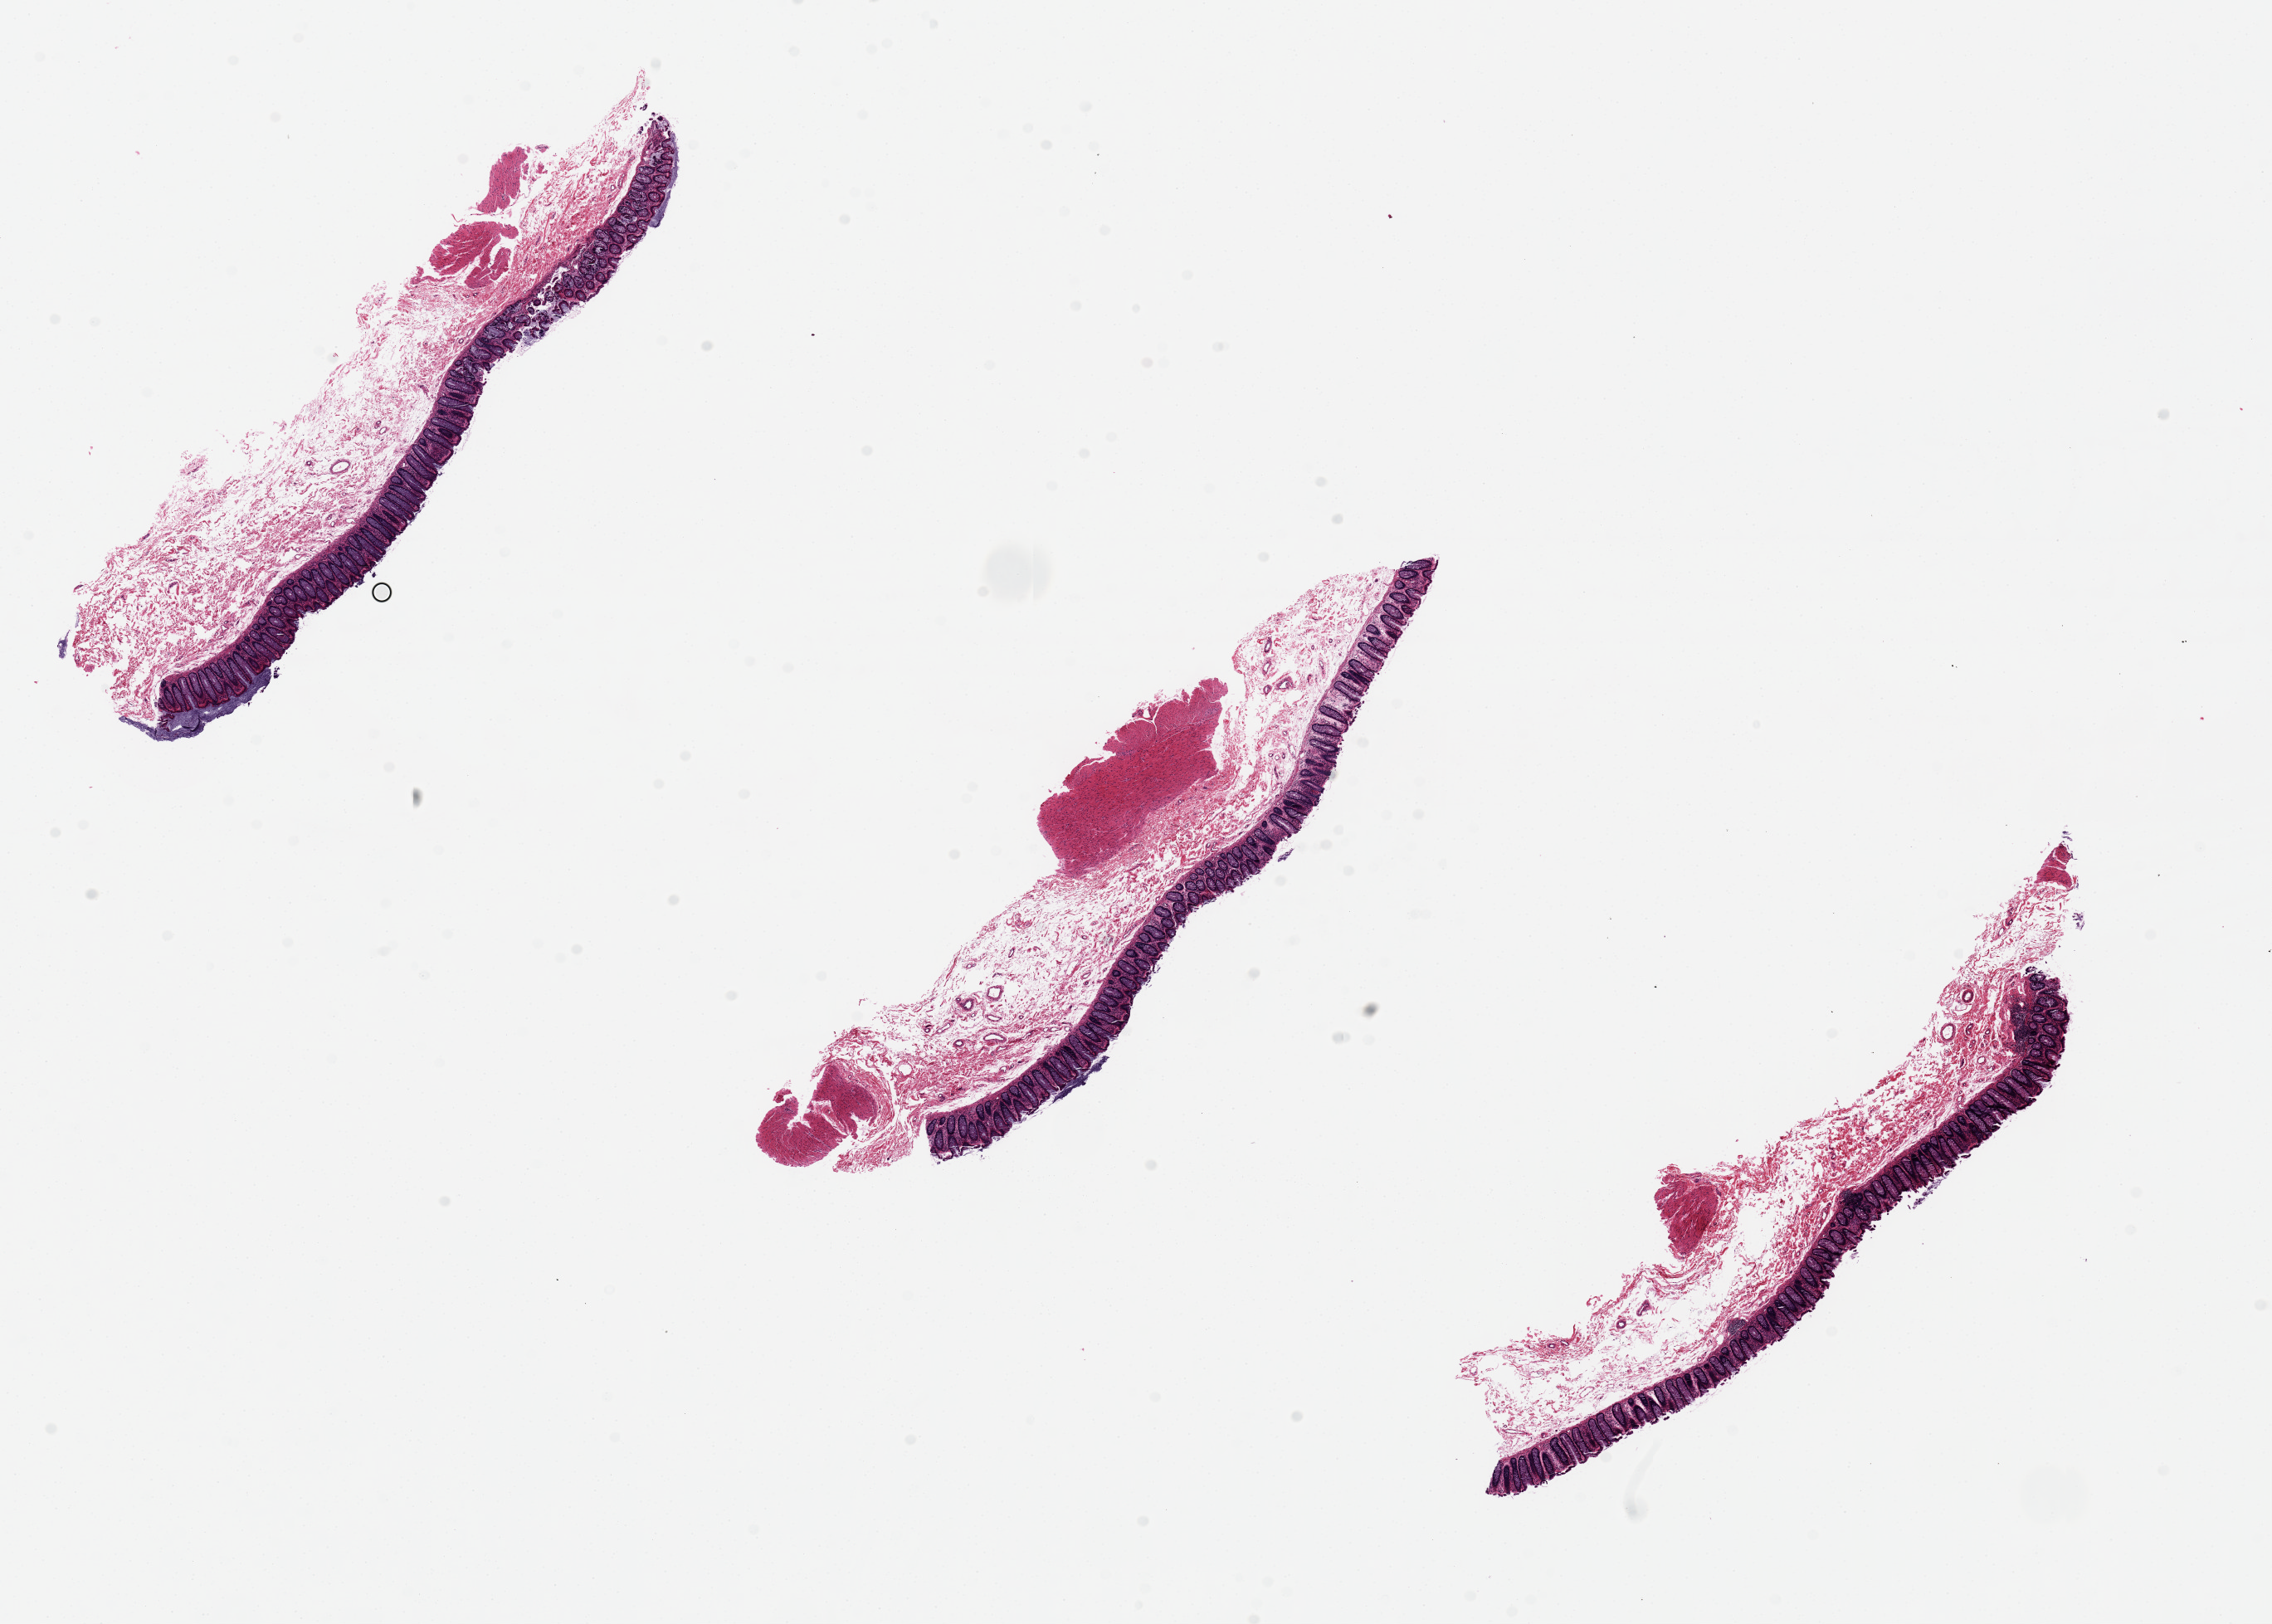
Whole-slide image, H&E stain, brightfield, shown as a low-resolution overview of the whole scanned area (about 21.7 x 15.5 mm, slide scanned at 20x). PAXgene-fixed paraffin-embedded (PFPE) section. Sampled site (target tissue): transverse colon. Donor tissue sample.
- review note (as recorded): superficial sloughing. Mucosa is ~20-23% specimen thickness